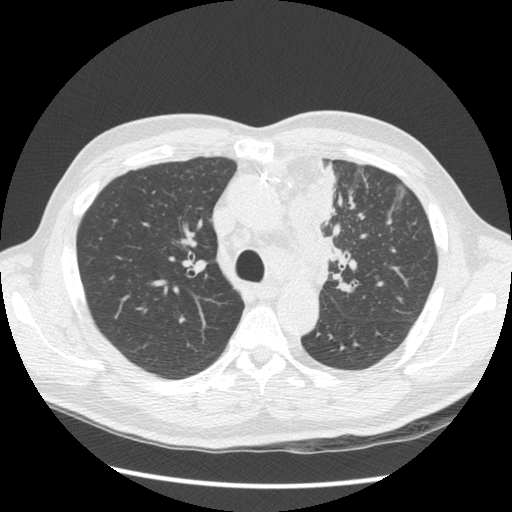
Low-dose screening chest CT, one axial slice. Slice 97 of 136 in the series (ordered by position). Reconstruction kernel STANDARD. 120 kVp. Lung window (W 1500 / L -600 HU). 2.5 mm slice thickness. 512 × 512 image matrix.
Structures marked on this image (manually delineated by an expert):
- lesion 1 (tumor, upper lobe of left lung): box from (x=288, y=154) to (x=333, y=287) px